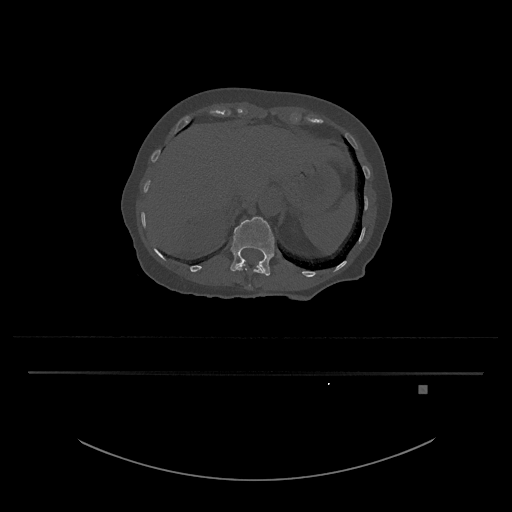
CT including the spine, one axial slice. Slice 576 of 797 in the series (ordered by position). 120 kVp. Bone window (W 1800 / L 400 HU). 0.5 mm slice thickness. 512 × 512 image matrix. Female patient, age 57 years. From the clinical record (not read from this slice): primary cancer: cervical.
Annotated regions visible in this slice (semi-automatic segmentation, software-assisted and operator-edited):
- L1 vertebra: bounding box <230,217,275,276> (left, top, right, bottom; pixels)
- T12 vertebra: <235,263,265,287>